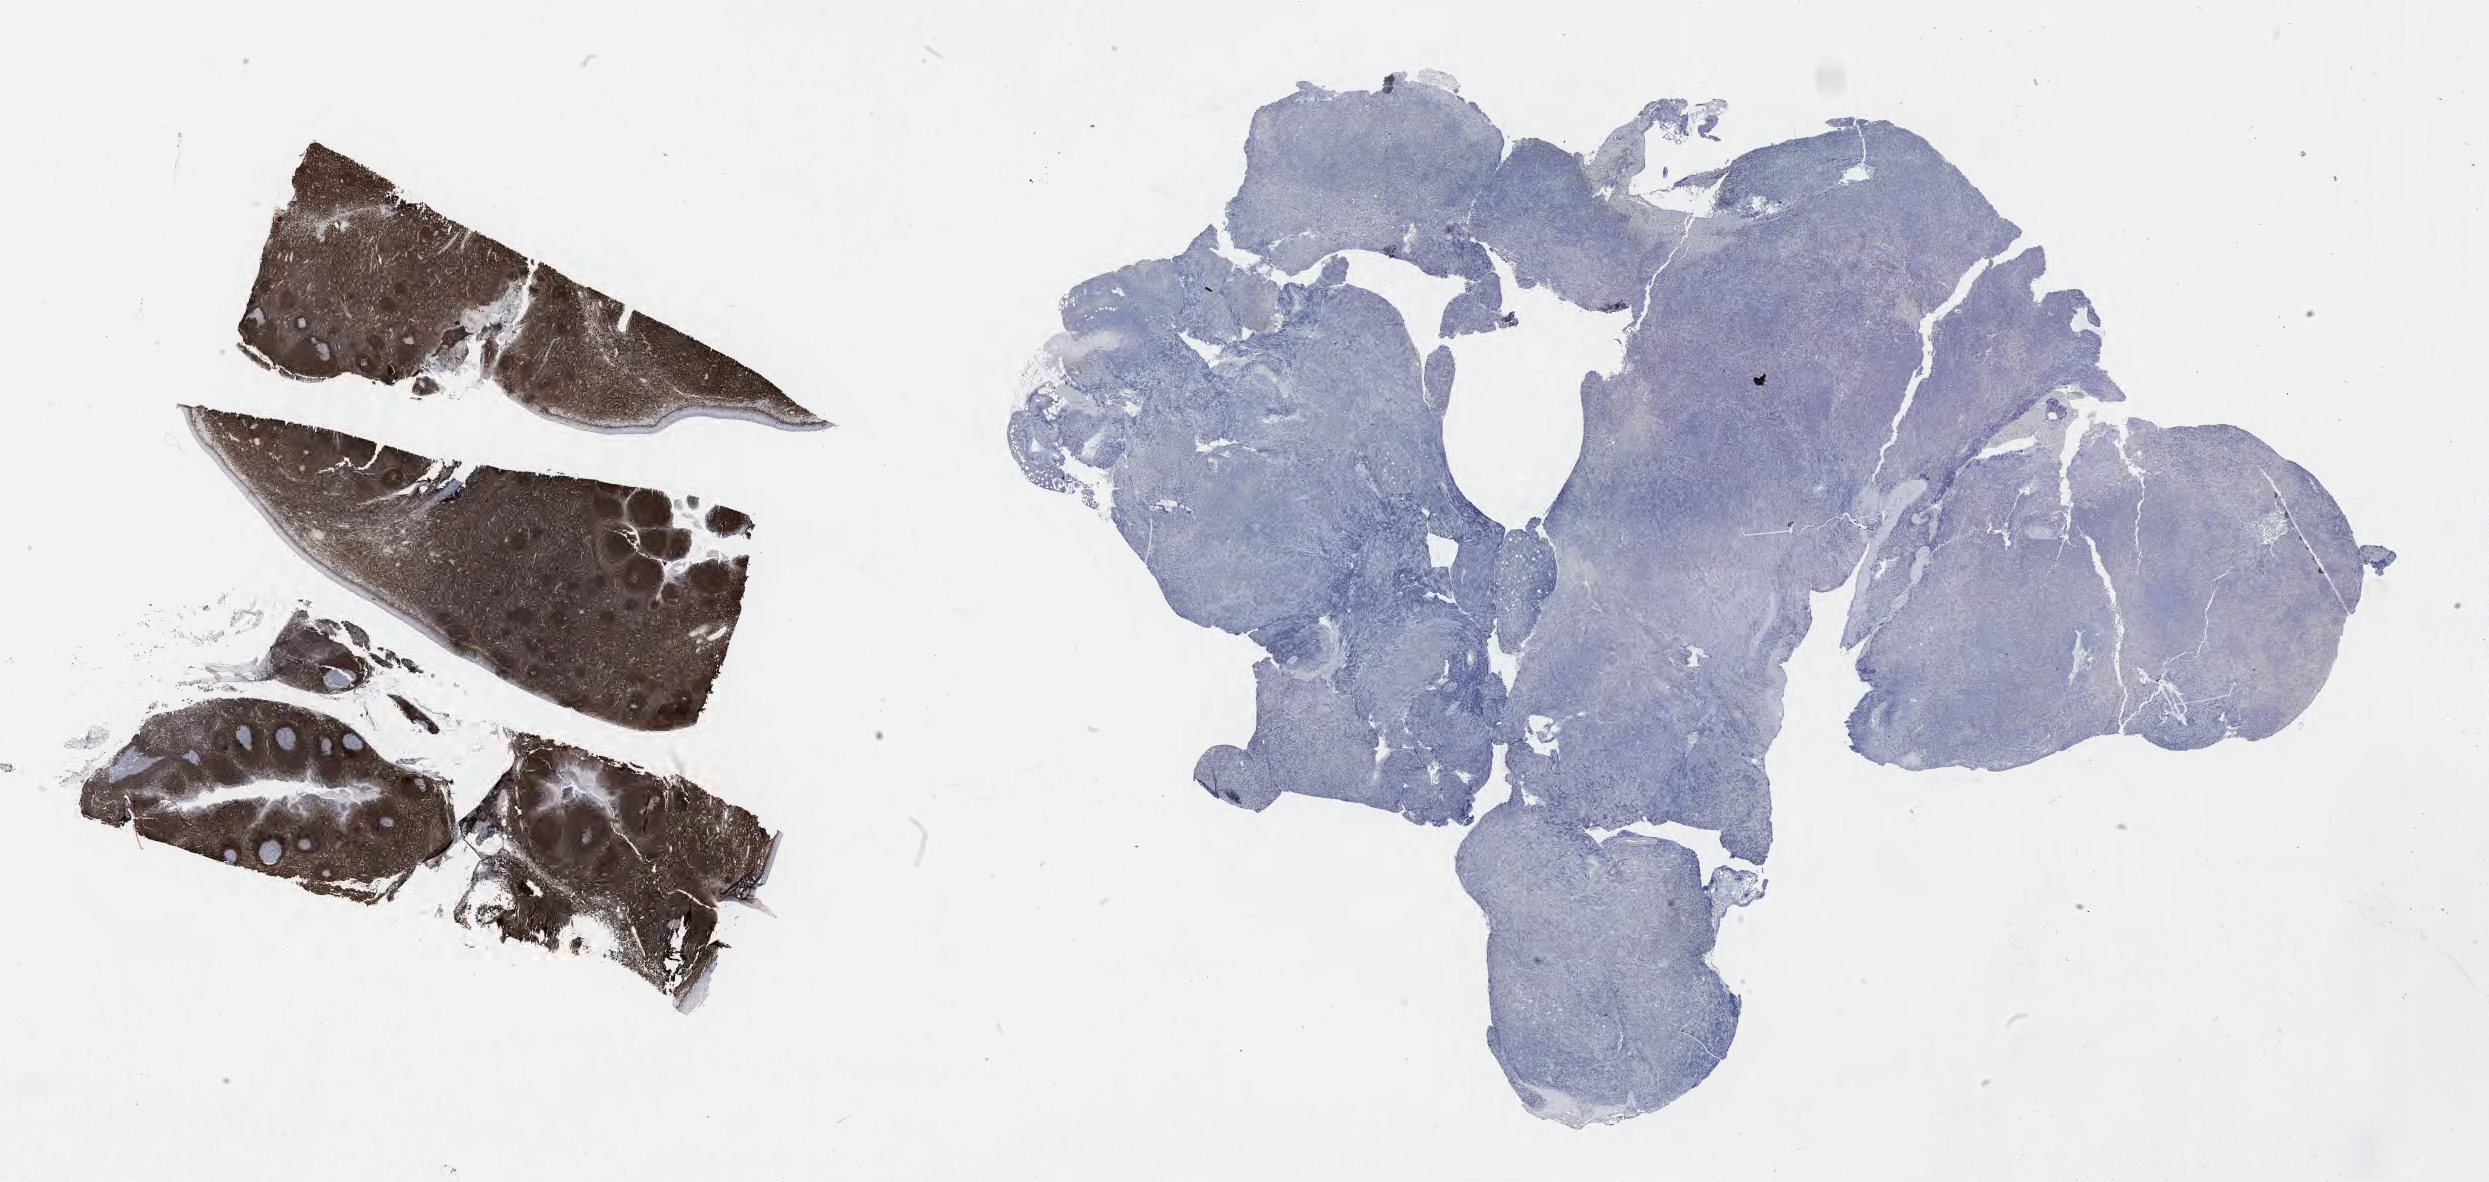
Whole-slide image, immunohistochemical stain for BCL2, a low-resolution overview of the entire scanned area, about 40.3 x 19.1 mm, specimen: tumor tissue, anatomic site: soft tissue of abdomen. Female patient; age at initial diagnosis 8 years.
Histologic diagnosis: Burkitt lymphoma, NOS.